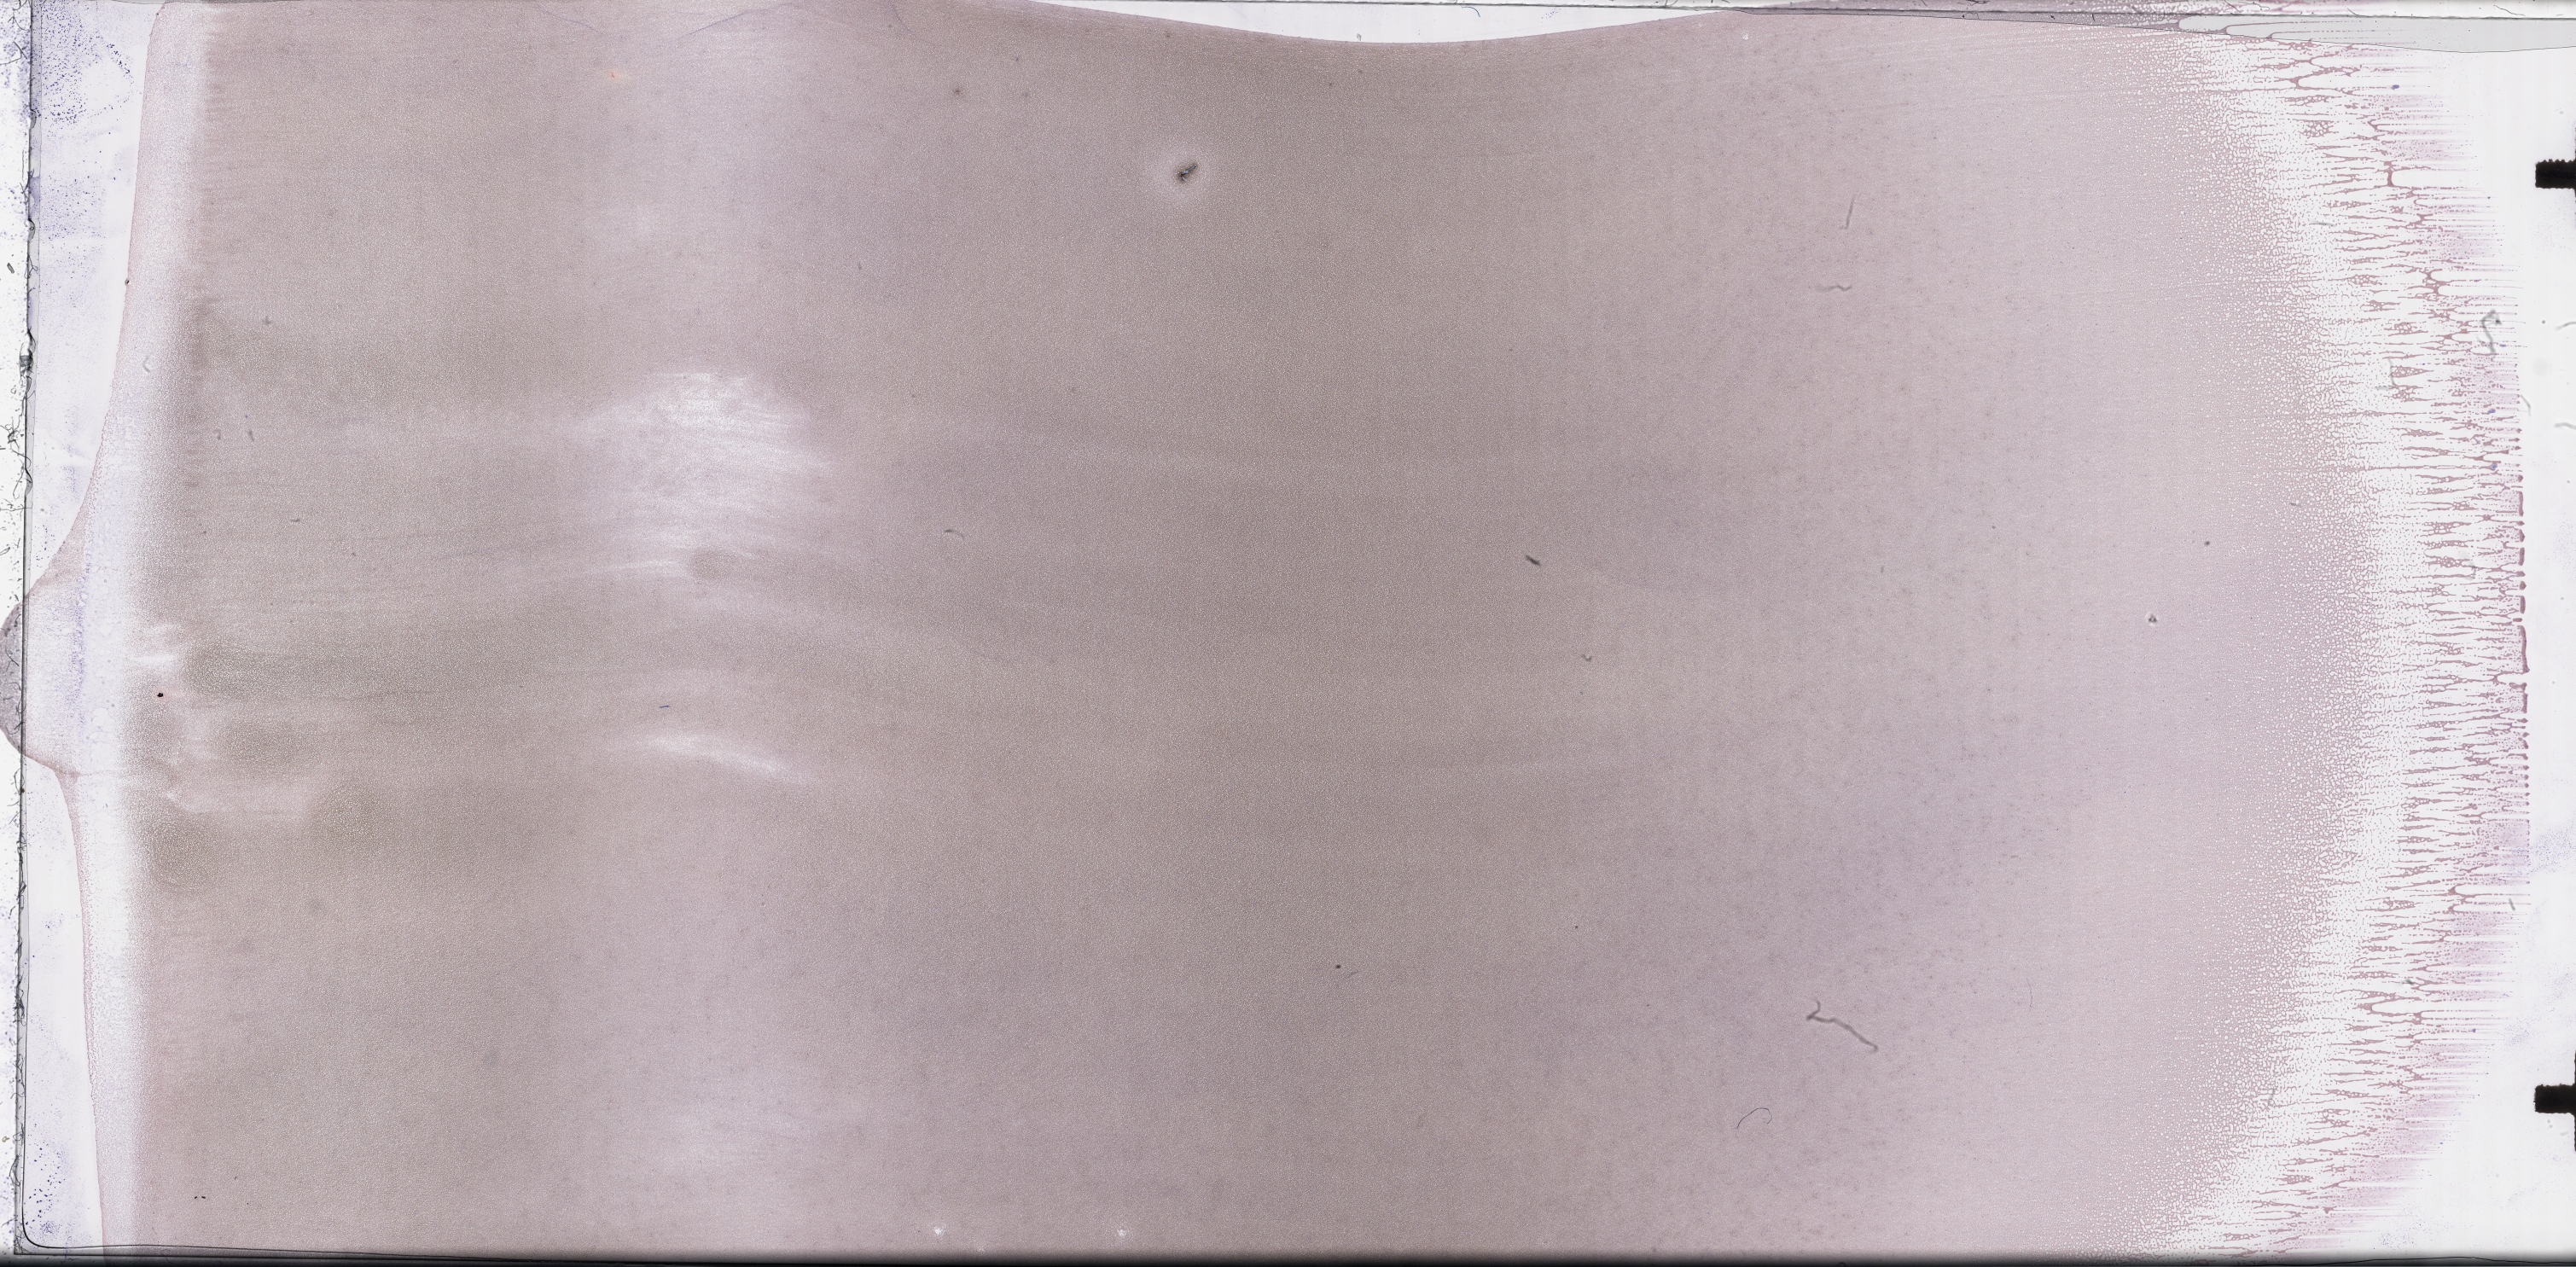
Whole-slide image of a whole blood smear, Wright–Giemsa stain — low-resolution overview of the scanned area, about 48.8 x 24.0 mm; specimen time point: collected on treatment. Patient sex: male.
• from a patient with: Plasma Cell Myeloma